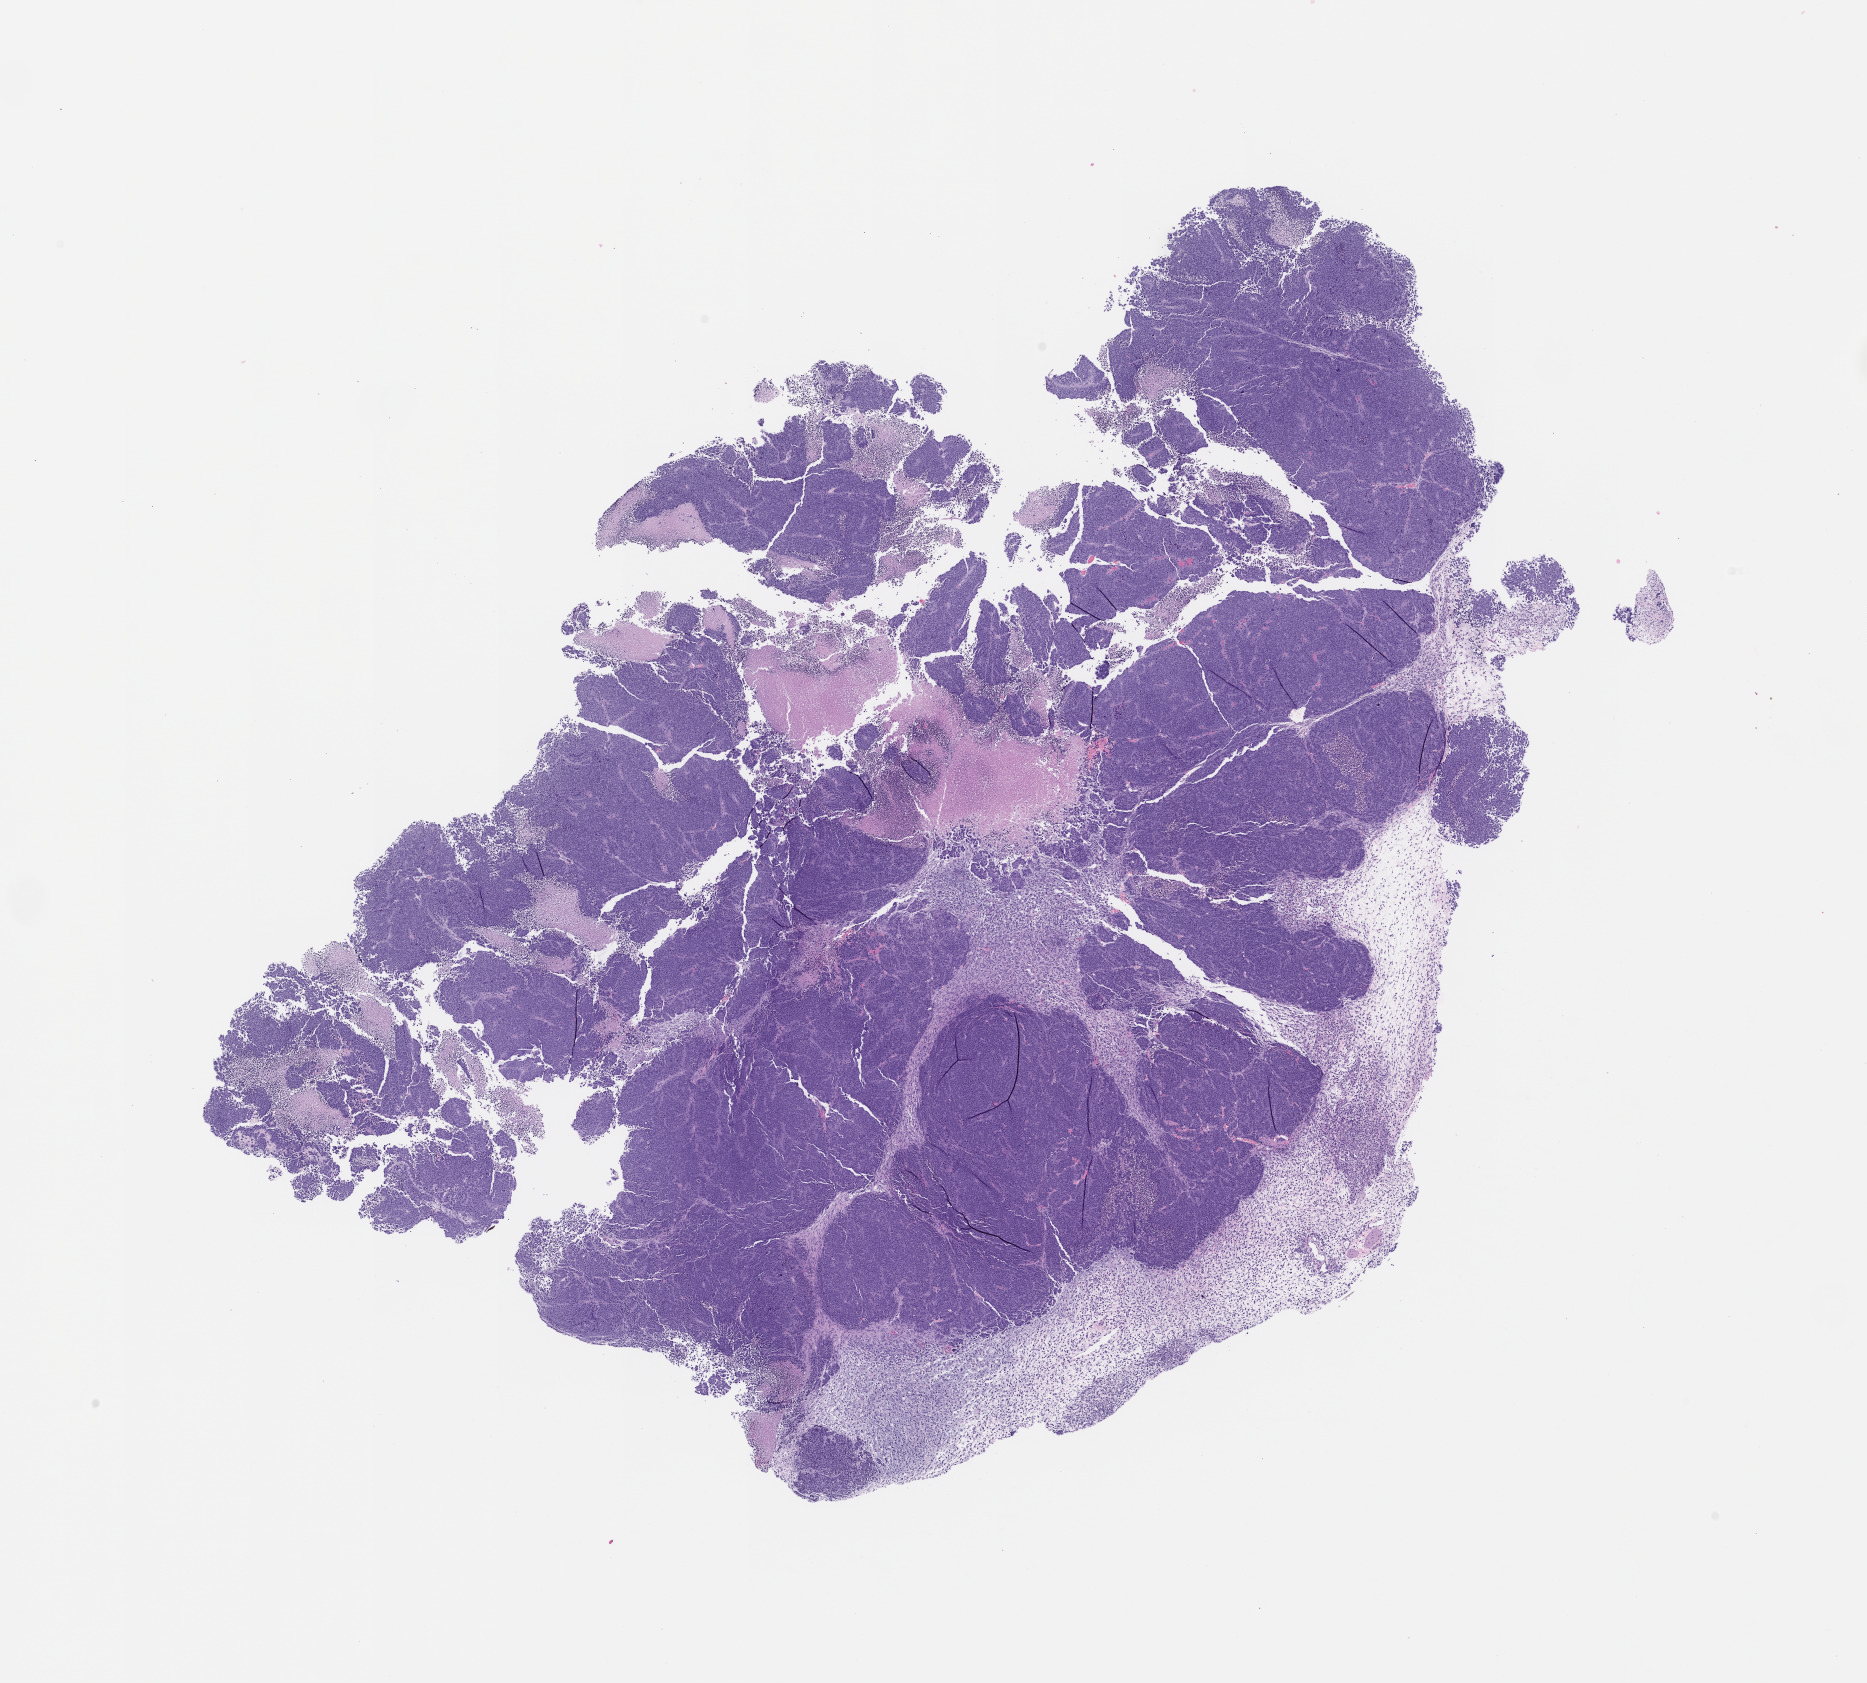
Hematoxylin and eosin (H&E) whole-slide image of a patient-derived xenograft (PDX) tumor grown in a mouse, passage 1, whole scanned area (about 15.0 x 13.5 mm) shown as a low-resolution overview, formalin-fixed paraffin-embedded section, originating tumor site category: bladder.
Originating patient diagnosis: Urothelial Carcinoma.